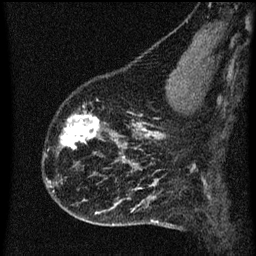
Breast MRI (dynamic contrast-enhanced), one sagittal slice; position 19 of 60 along the scan axis; dynamic contrast-enhanced series, image 2 of 3 at this slice position (ordered by acquisition); 1.5 T; TE 4.2 ms, TR 8 ms; 256 × 256 image matrix, field of view 180 × 180 mm. Female patient, age 43 years.
Structures marked on this image (semi-automatic segmentation, software-assisted and operator-edited):
- analysis volume of interest (the breast-tissue region the enhancement analysis was run in; not a lesion): bounding box [x1, y1, x2, y2] px = [55, 104, 104, 153]
- tumour enhancement mask (voxels above the 70 % enhancement threshold inside the analysis volume of interest): [60, 112, 103, 149]